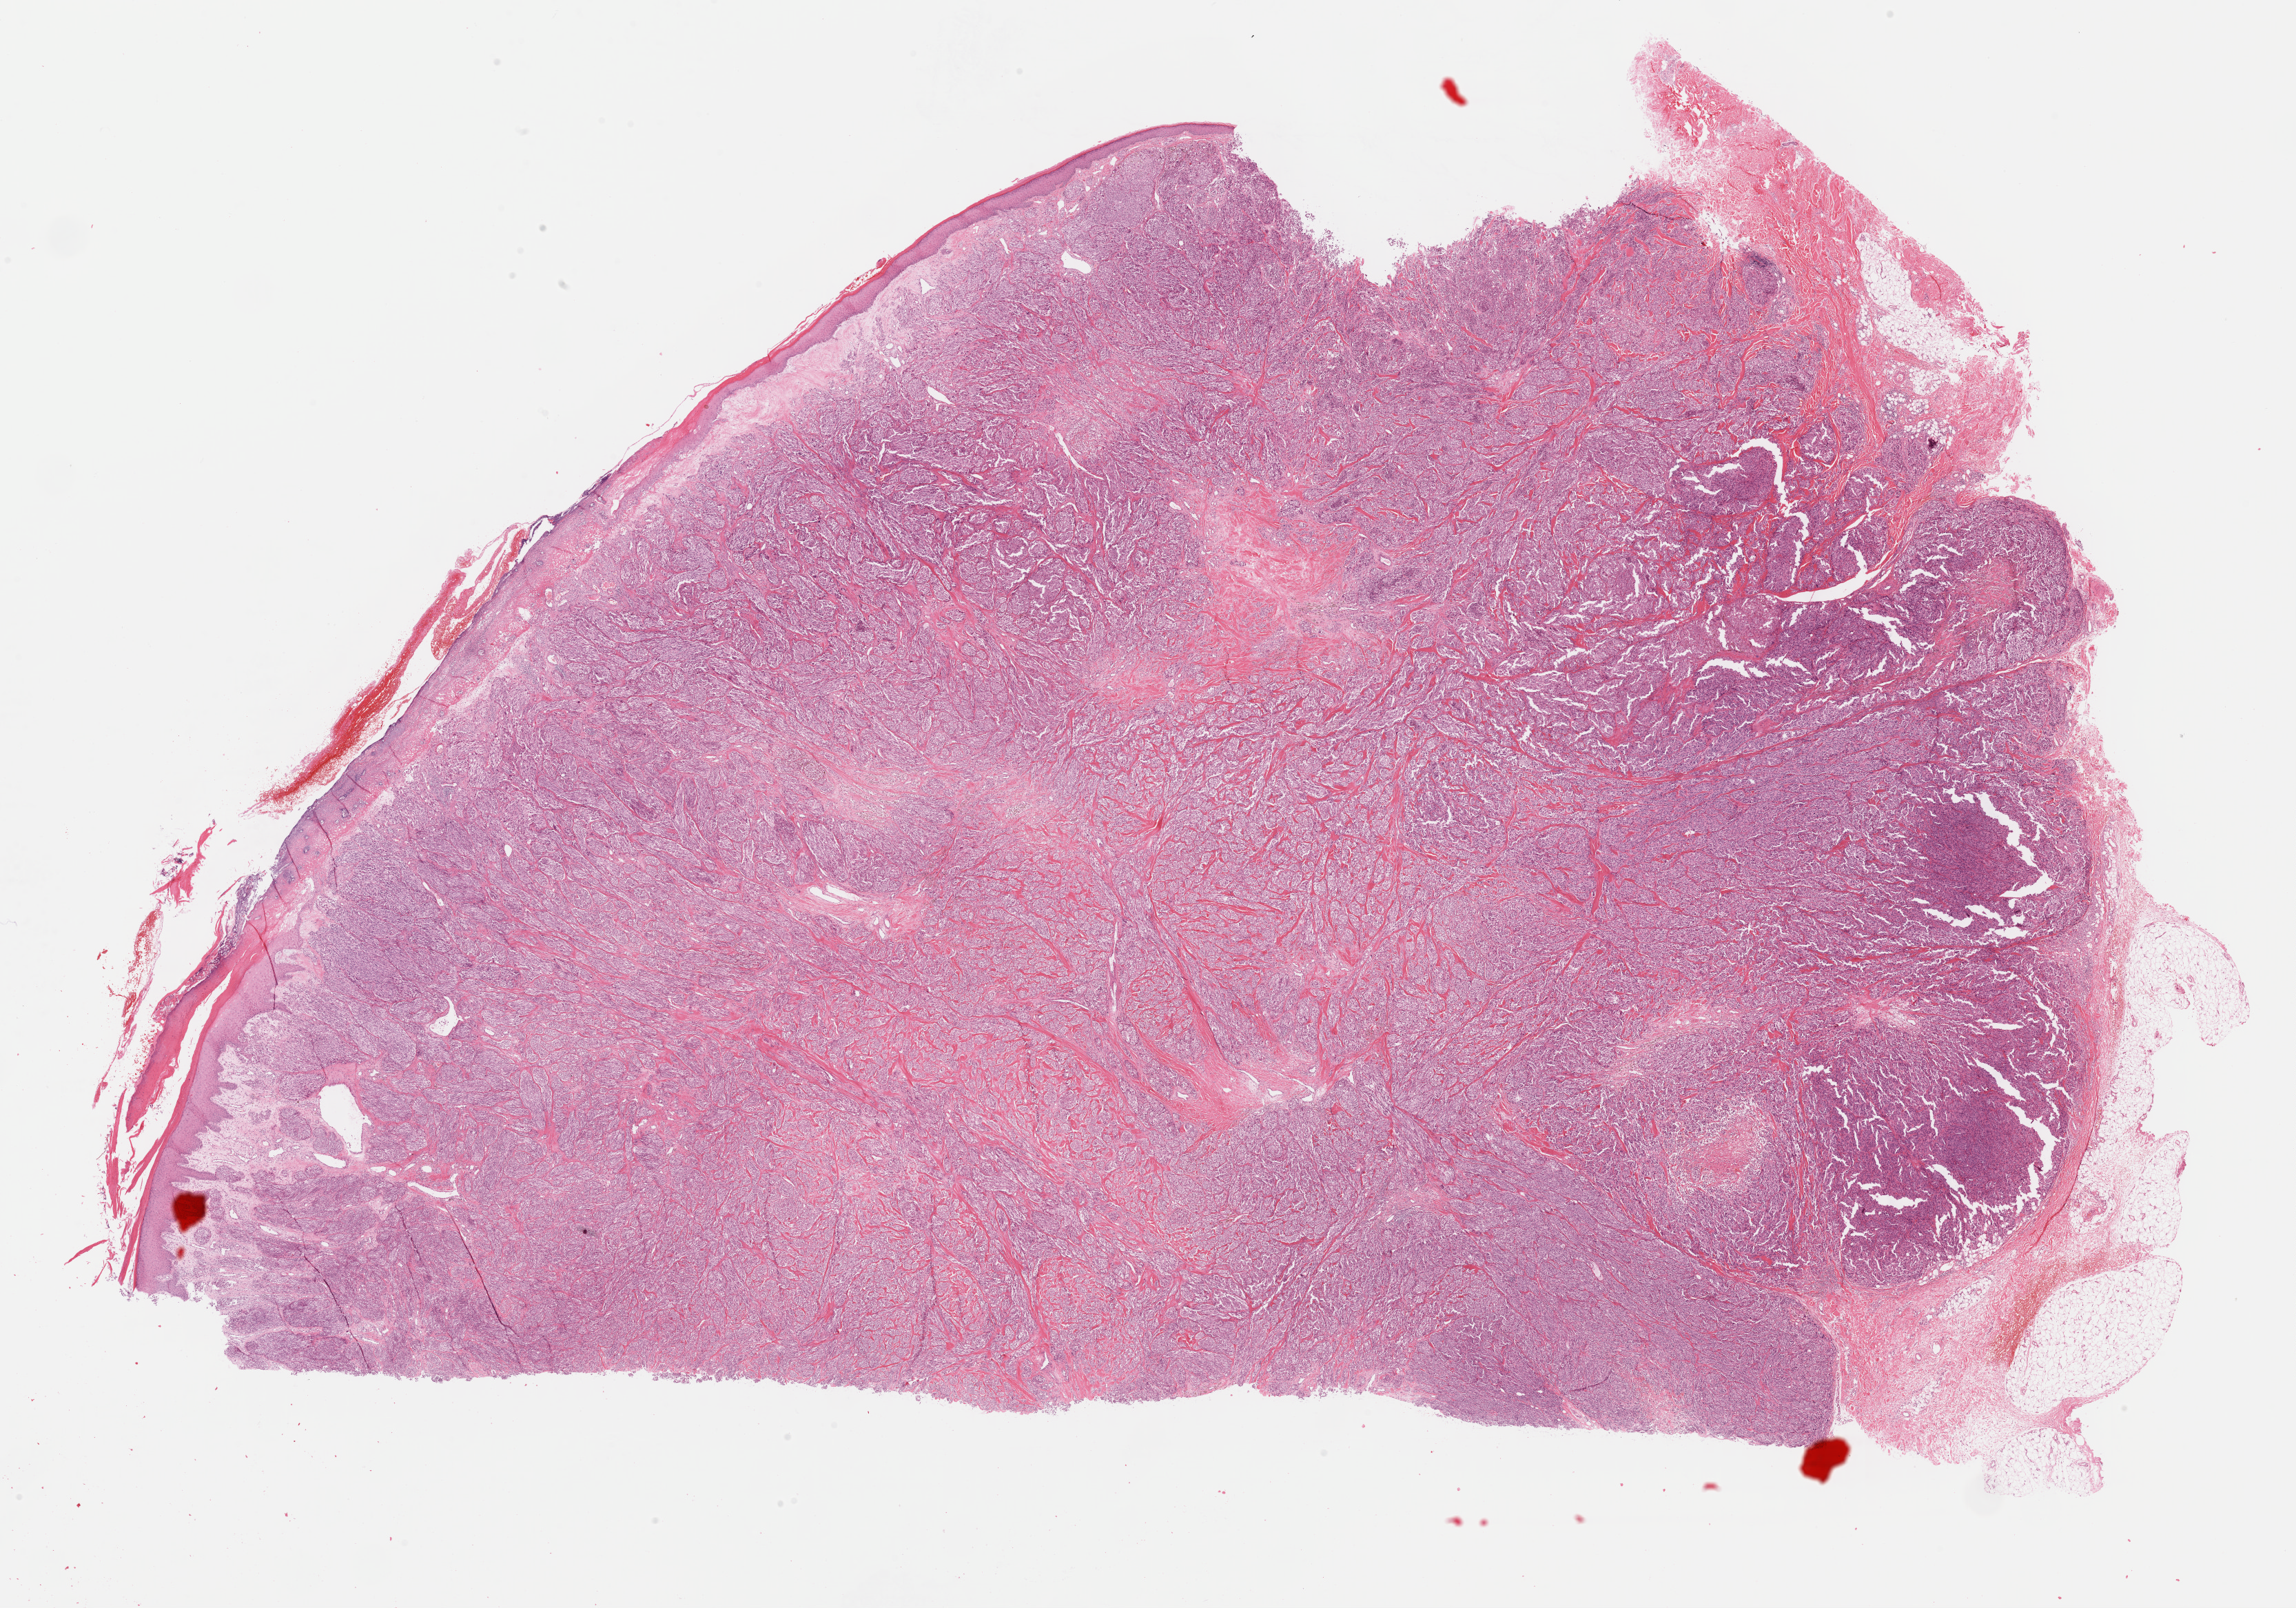
H&E-stained whole-slide image — low-resolution overview of the scanned area, about 26.3 x 18.4 mm (from a 40x scan); FFPE section; skin, primary tumour sample. Male patient; age at initial diagnosis 56 years.
Histologic diagnosis: Malignant melanoma, NOS.